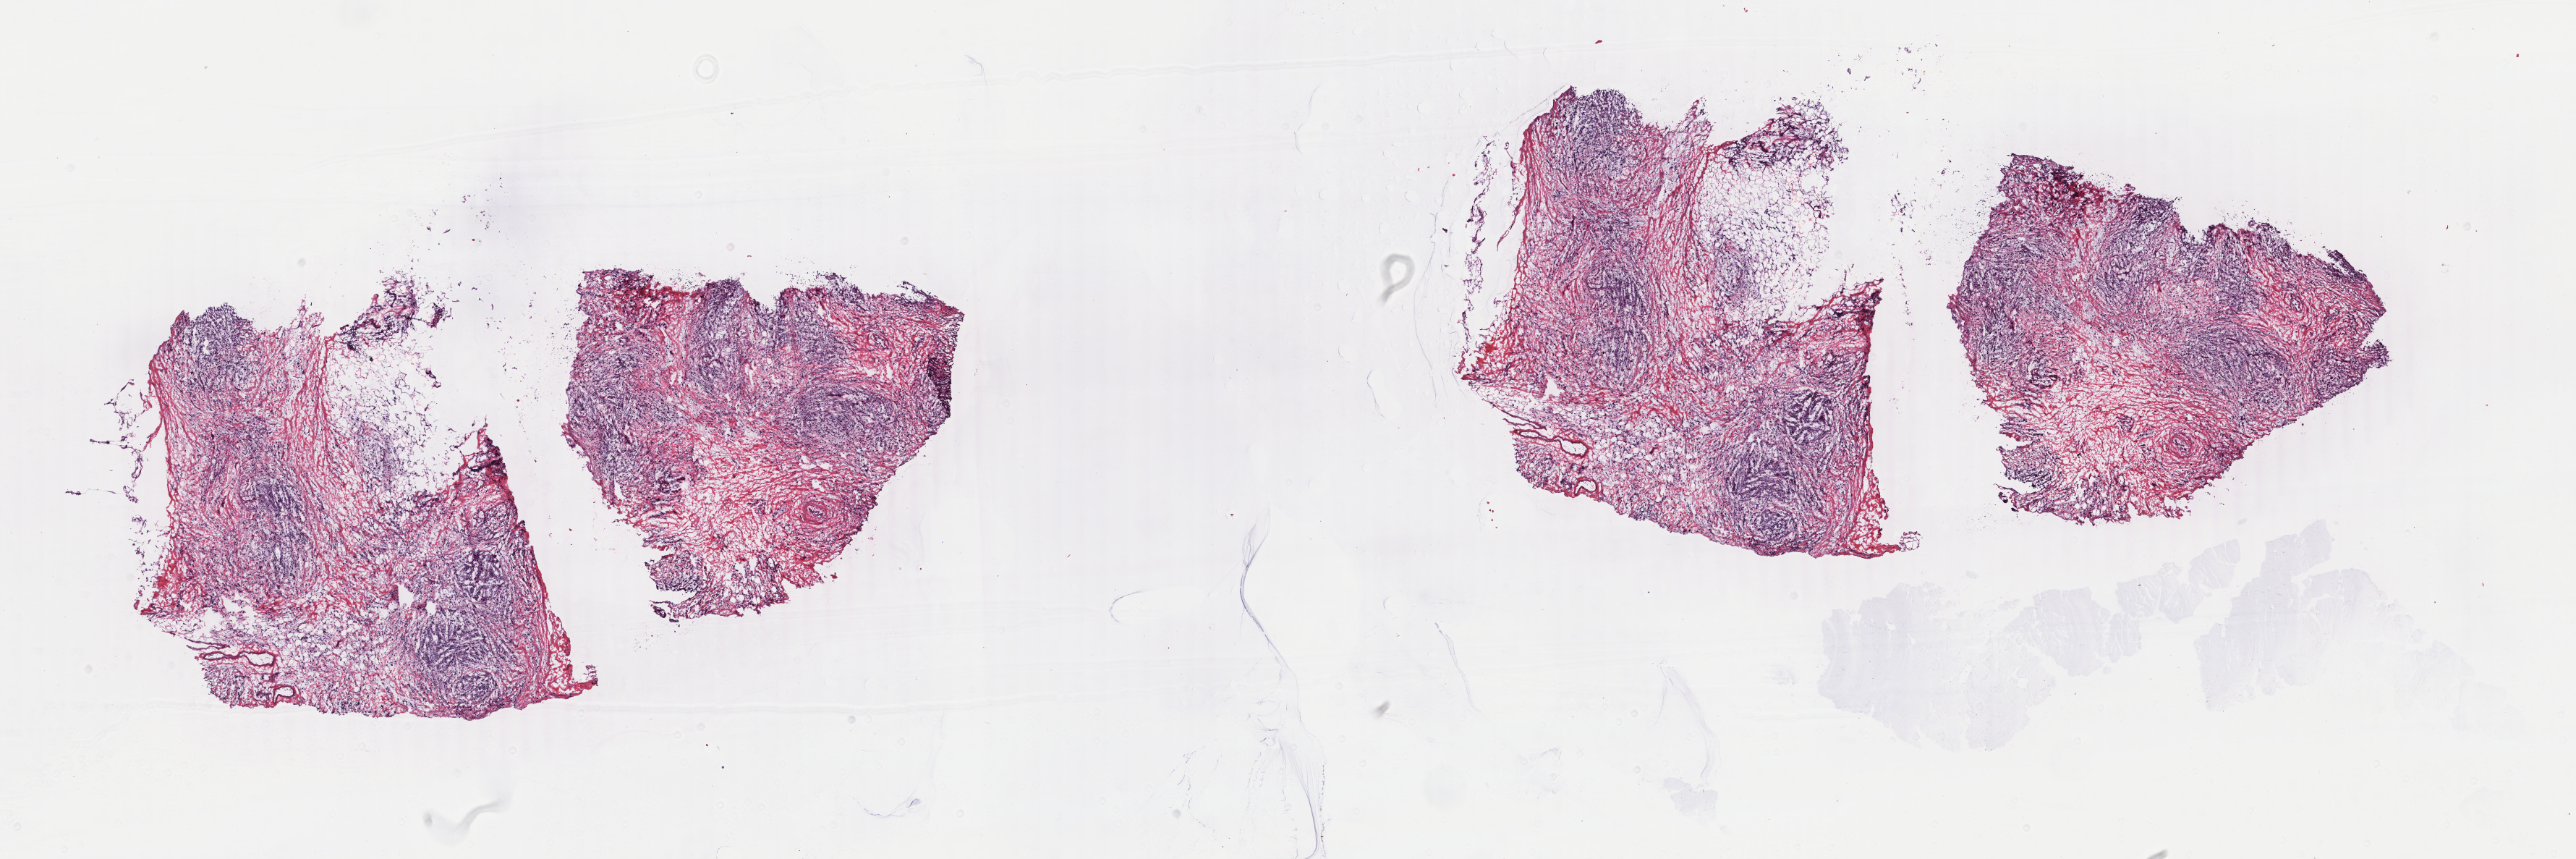
H&E-stained whole-slide image, shown as a low-resolution overview of the whole scanned area (about 28.3 x 9.4 mm, slide scanned at 40x); frozen section from the top of the tissue portion; breast, primary tumour sample. Patient: female, age at initial diagnosis 38 years. Slide review estimates, as recorded: tumour cells 80%, tumour nuclei 80%, normal cells 0%, stromal cells 18%, necrosis 2%. Inflammatory infiltration, as recorded: lymphocyte infiltration 1%, monocyte infiltration 0%, neutrophil infiltration 0%.
* TNM: T3 N1b M0
* diagnosis: Lobular carcinoma, NOS
* lymph nodes positive (case pathology): 6 of 24 examined
* laterality: left
* AJCC pathologic stage: IIIA (4th edition)